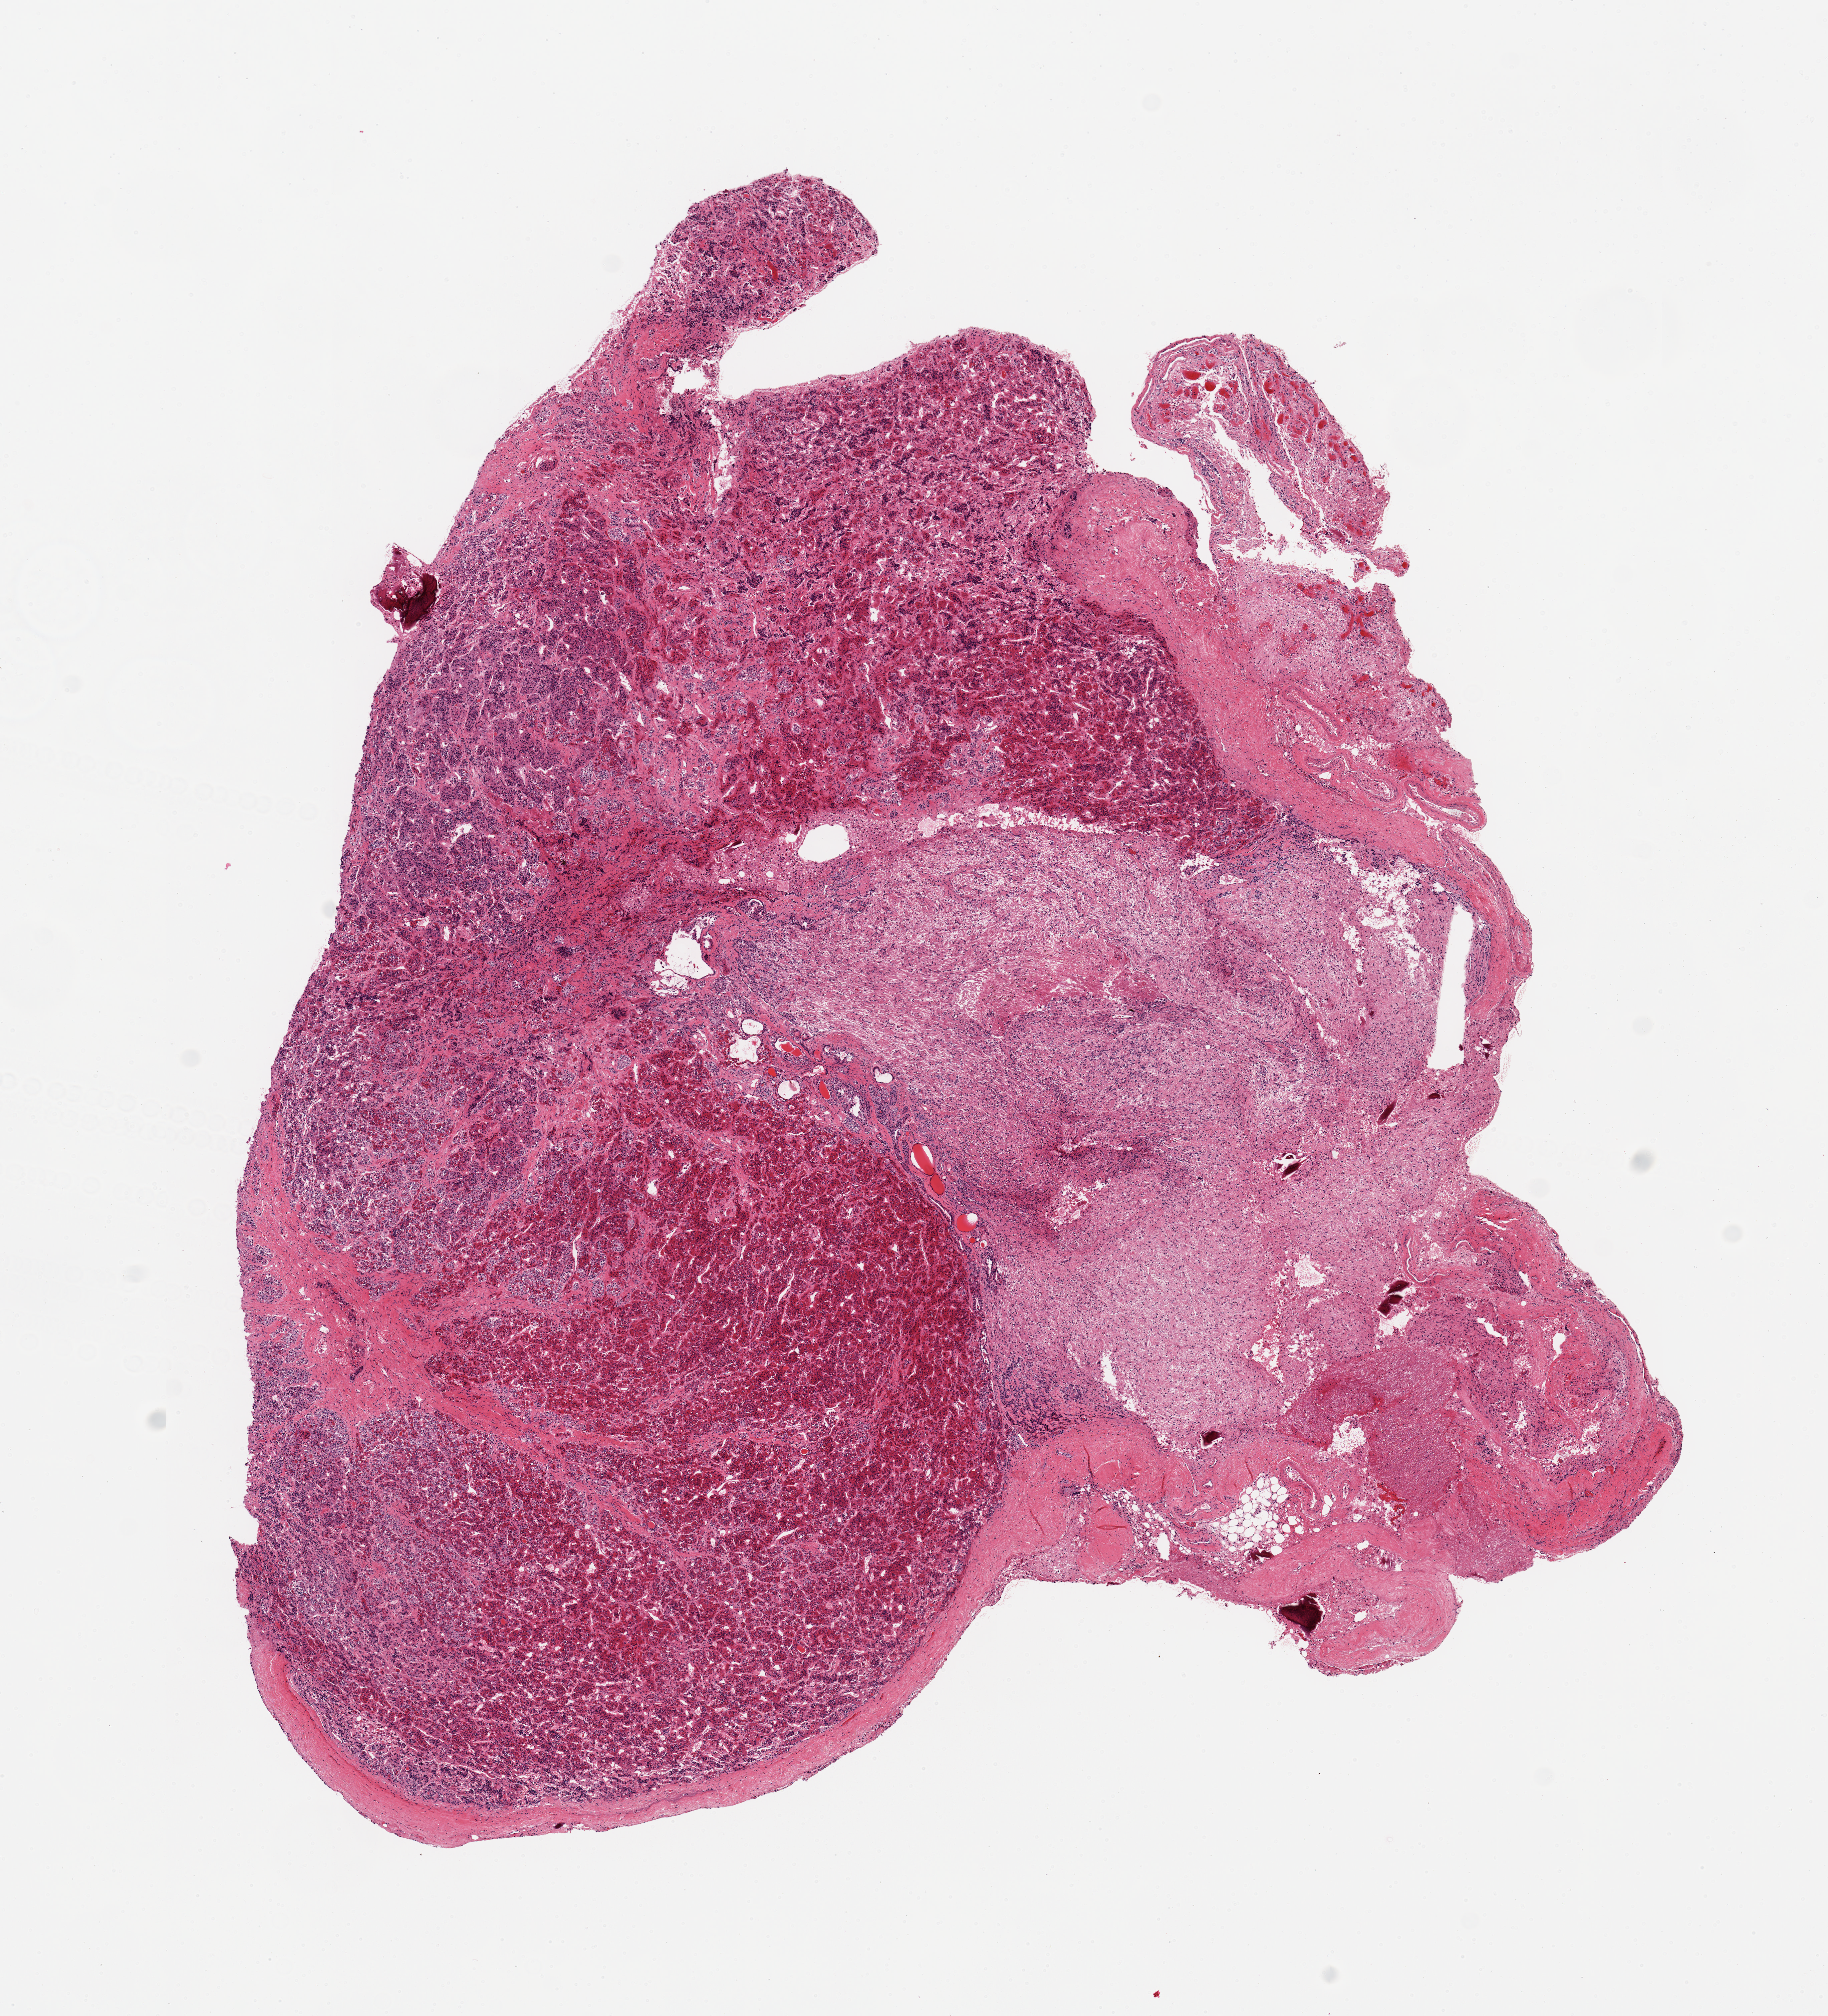
Digitized hematoxylin and eosin (H&E)-stained section — low-resolution overview of the scanned area, about 10.8 x 11.9 mm; PAXgene-fixed paraffin-embedded (PFPE) section; section of pituitary (target tissue); donor tissue sample. Donor: male.
Review note (as recorded): 1 piece; both anterior and posterior portions represented.